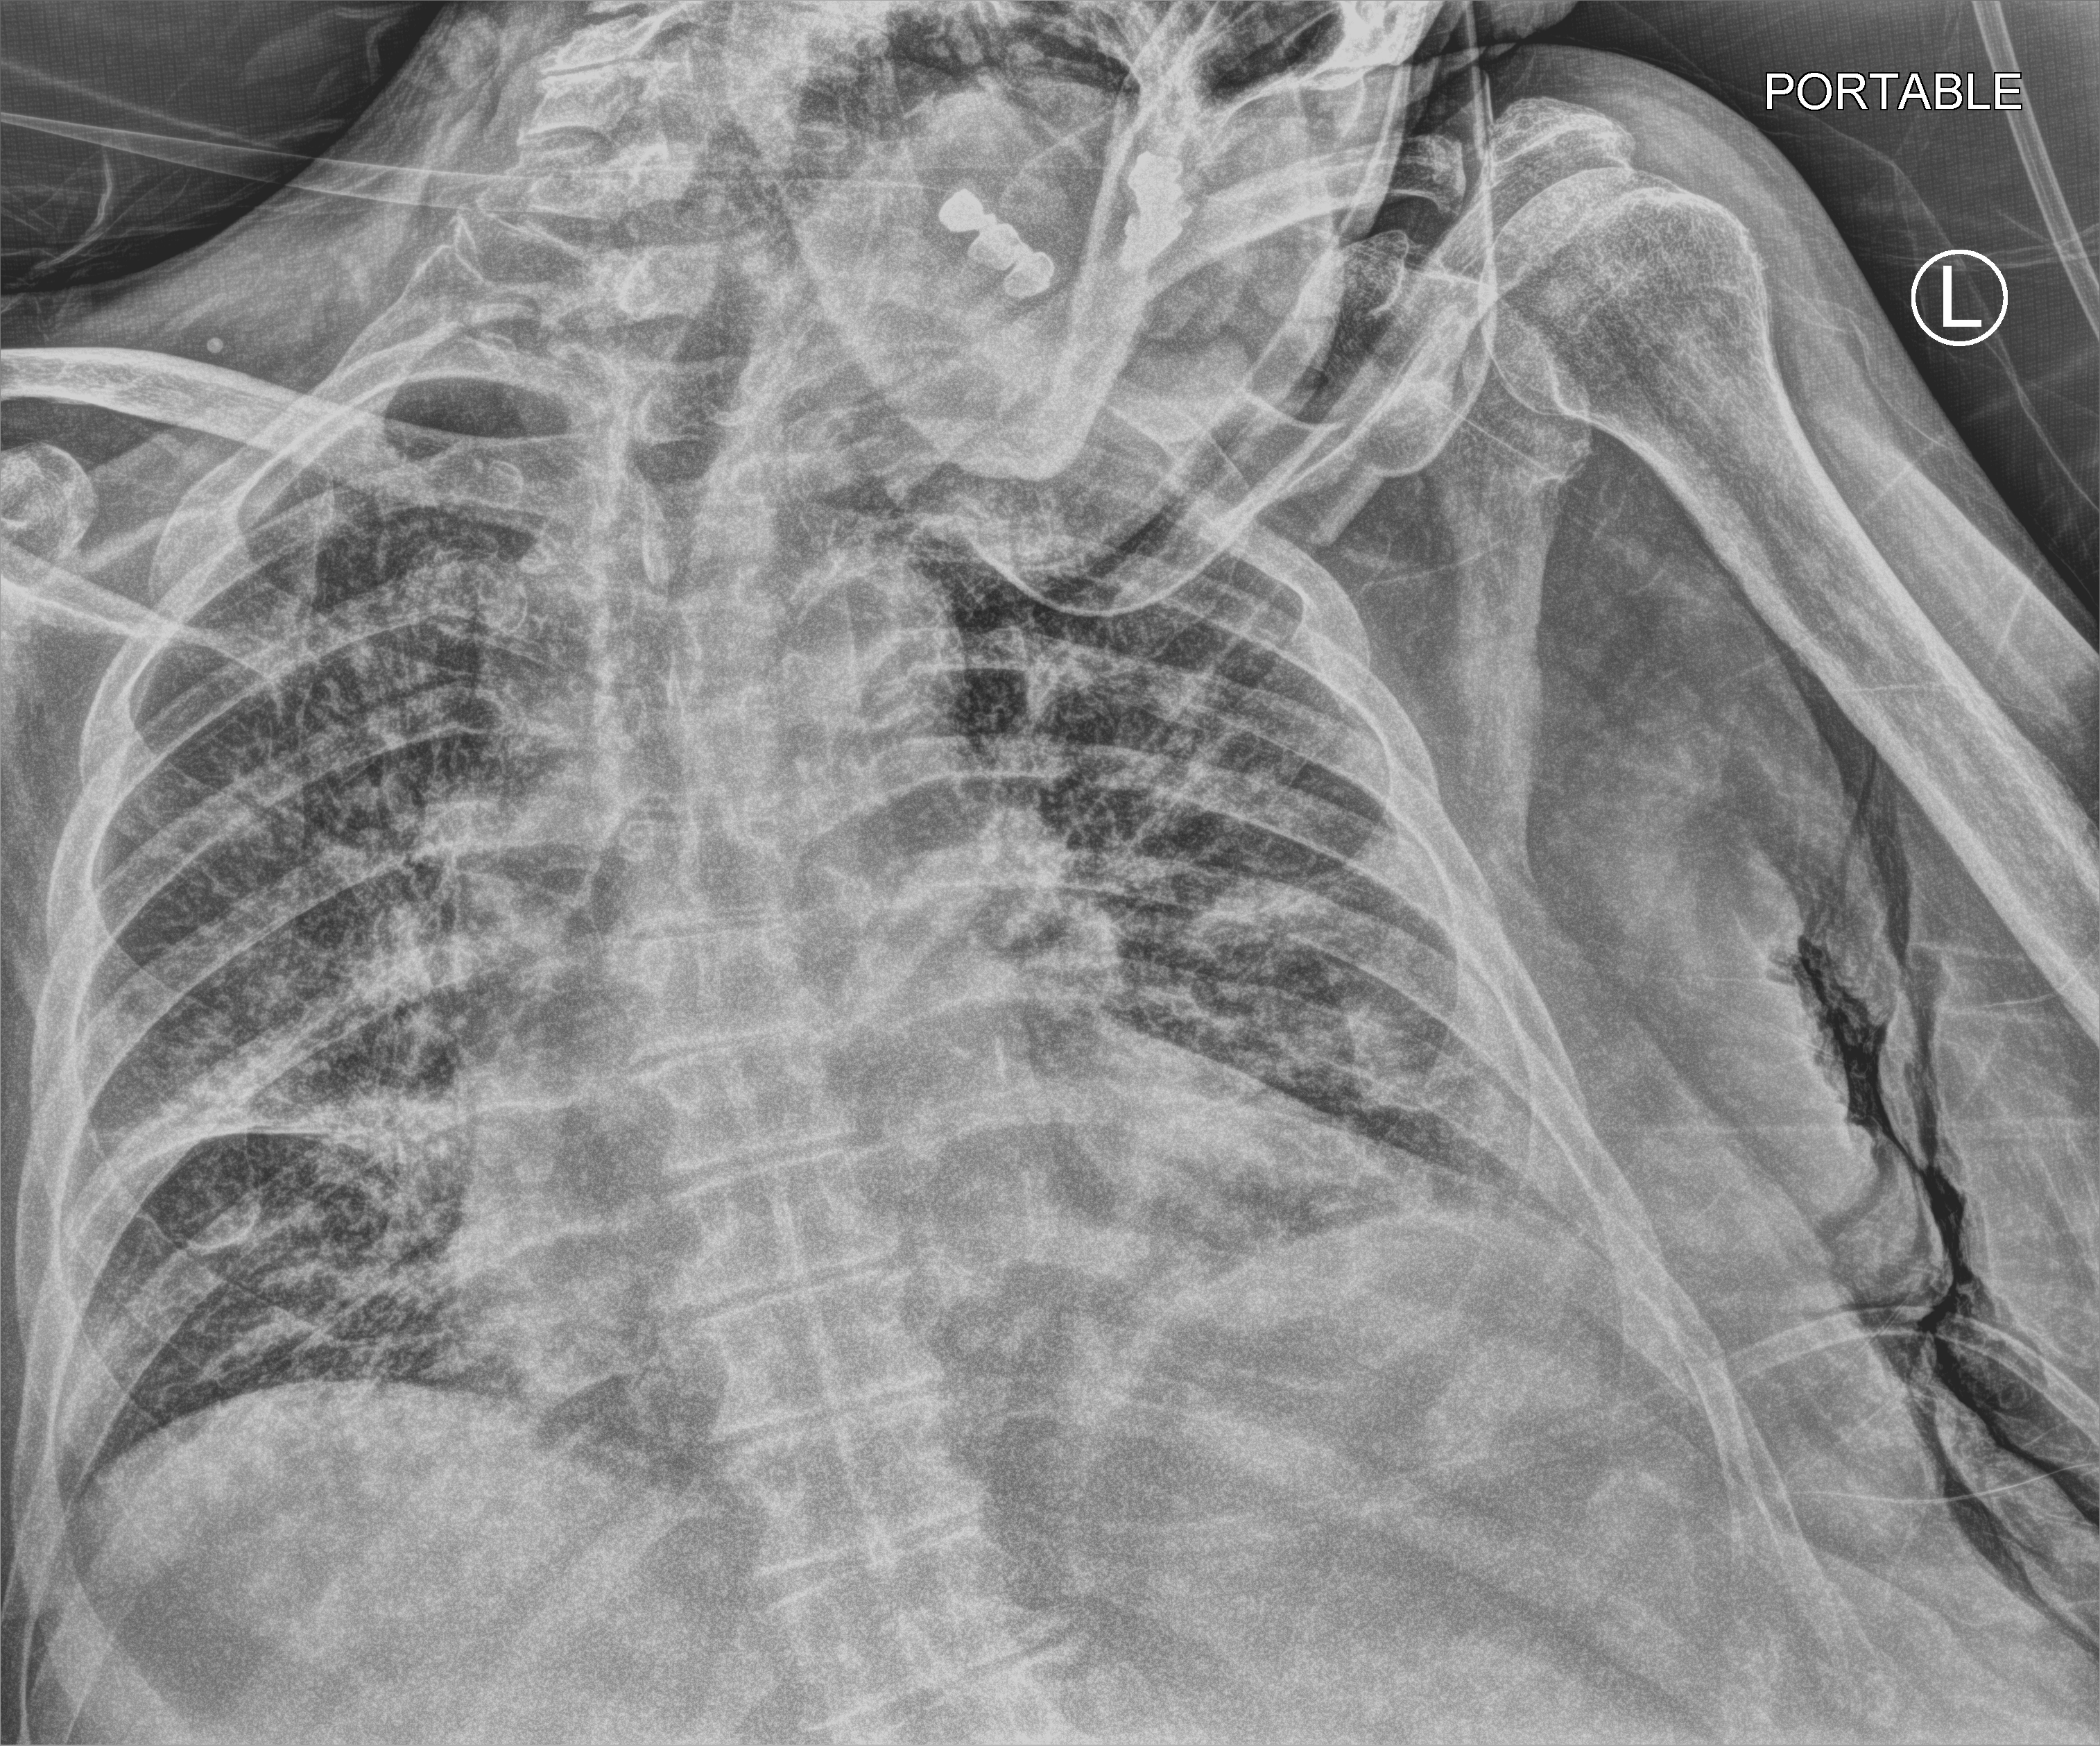
Portable chest radiograph; anteroposterior (AP) projection. Patient hospitalised with COVID-19; male, aged 75–90 years.
Admission-level facts for this patient (not findings on this image; timing relative to this image not recorded):
- admitted to intensive care during this hospital stay: no